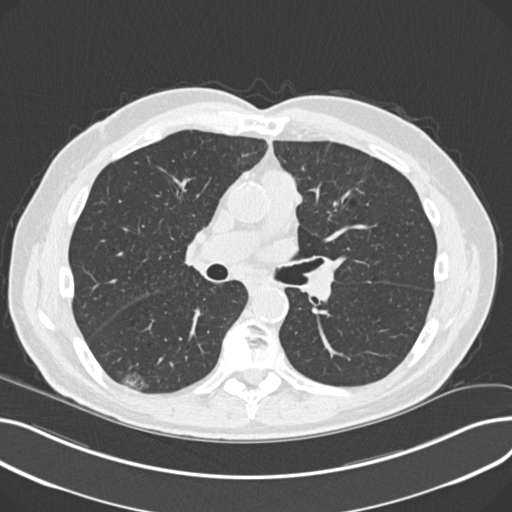
Axial slice from a low-dose chest CT screening exam, third annual screen, lung window (W 1500 / L -600 HU), slice 108 of 230 in the series. Male participant, aged 68 years at enrolment. Current smoker at enrolment.
Lesion marked by an expert reader, bounding box <122,366,159,398> (left, top, right, bottom; pixels). The screening reader recorded 5 non-calcified nodules or masses ≥4 mm on this exam (right upper lobe, left upper lobe, right upper lobe, right lower lobe, right upper lobe); which of them this box marks is not recorded. Lung cancer was diagnosed 247 days after this screen: non-small cell carcinoma, right lower lobe, poorly differentiated (G3), stage IA (AJCC 6th edition), 23 mm at pathology.